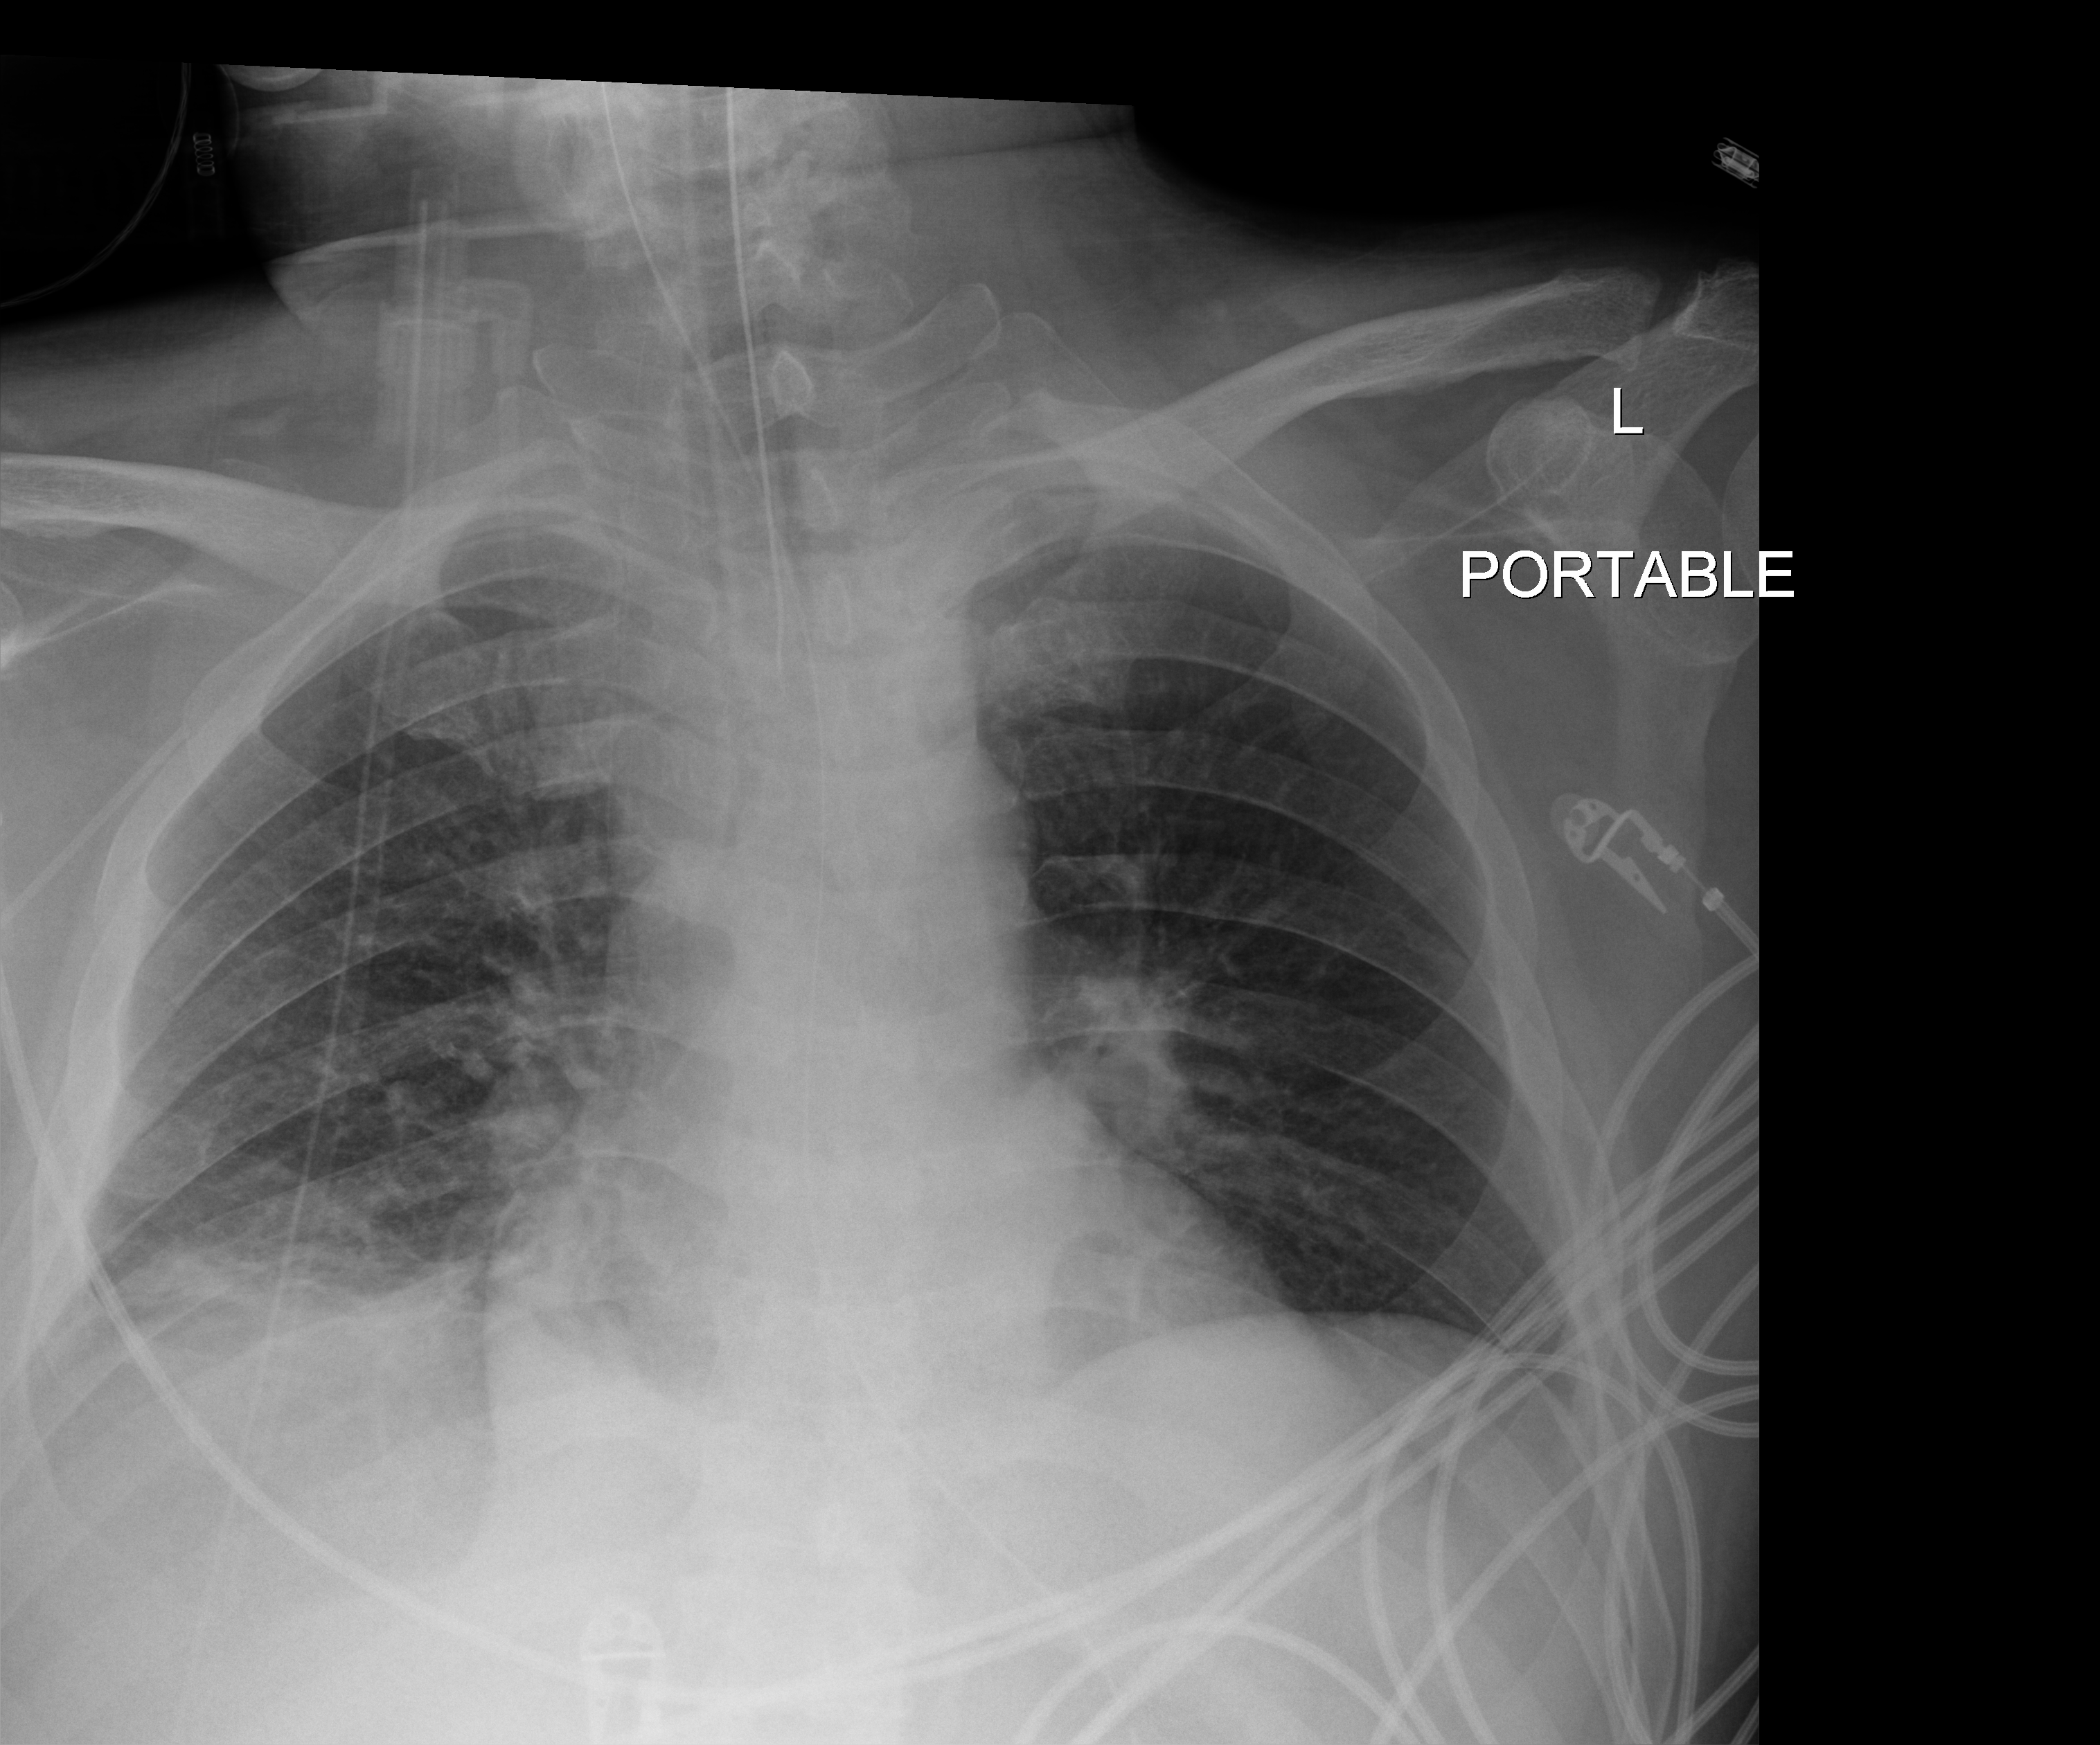
Chest X-ray (portable). Male patient hospitalised with COVID-19, age 18–59 years.
Admission-level facts for this patient (not findings on this image; timing relative to this image not recorded):
- admitted to intensive care during this hospital stay: yes